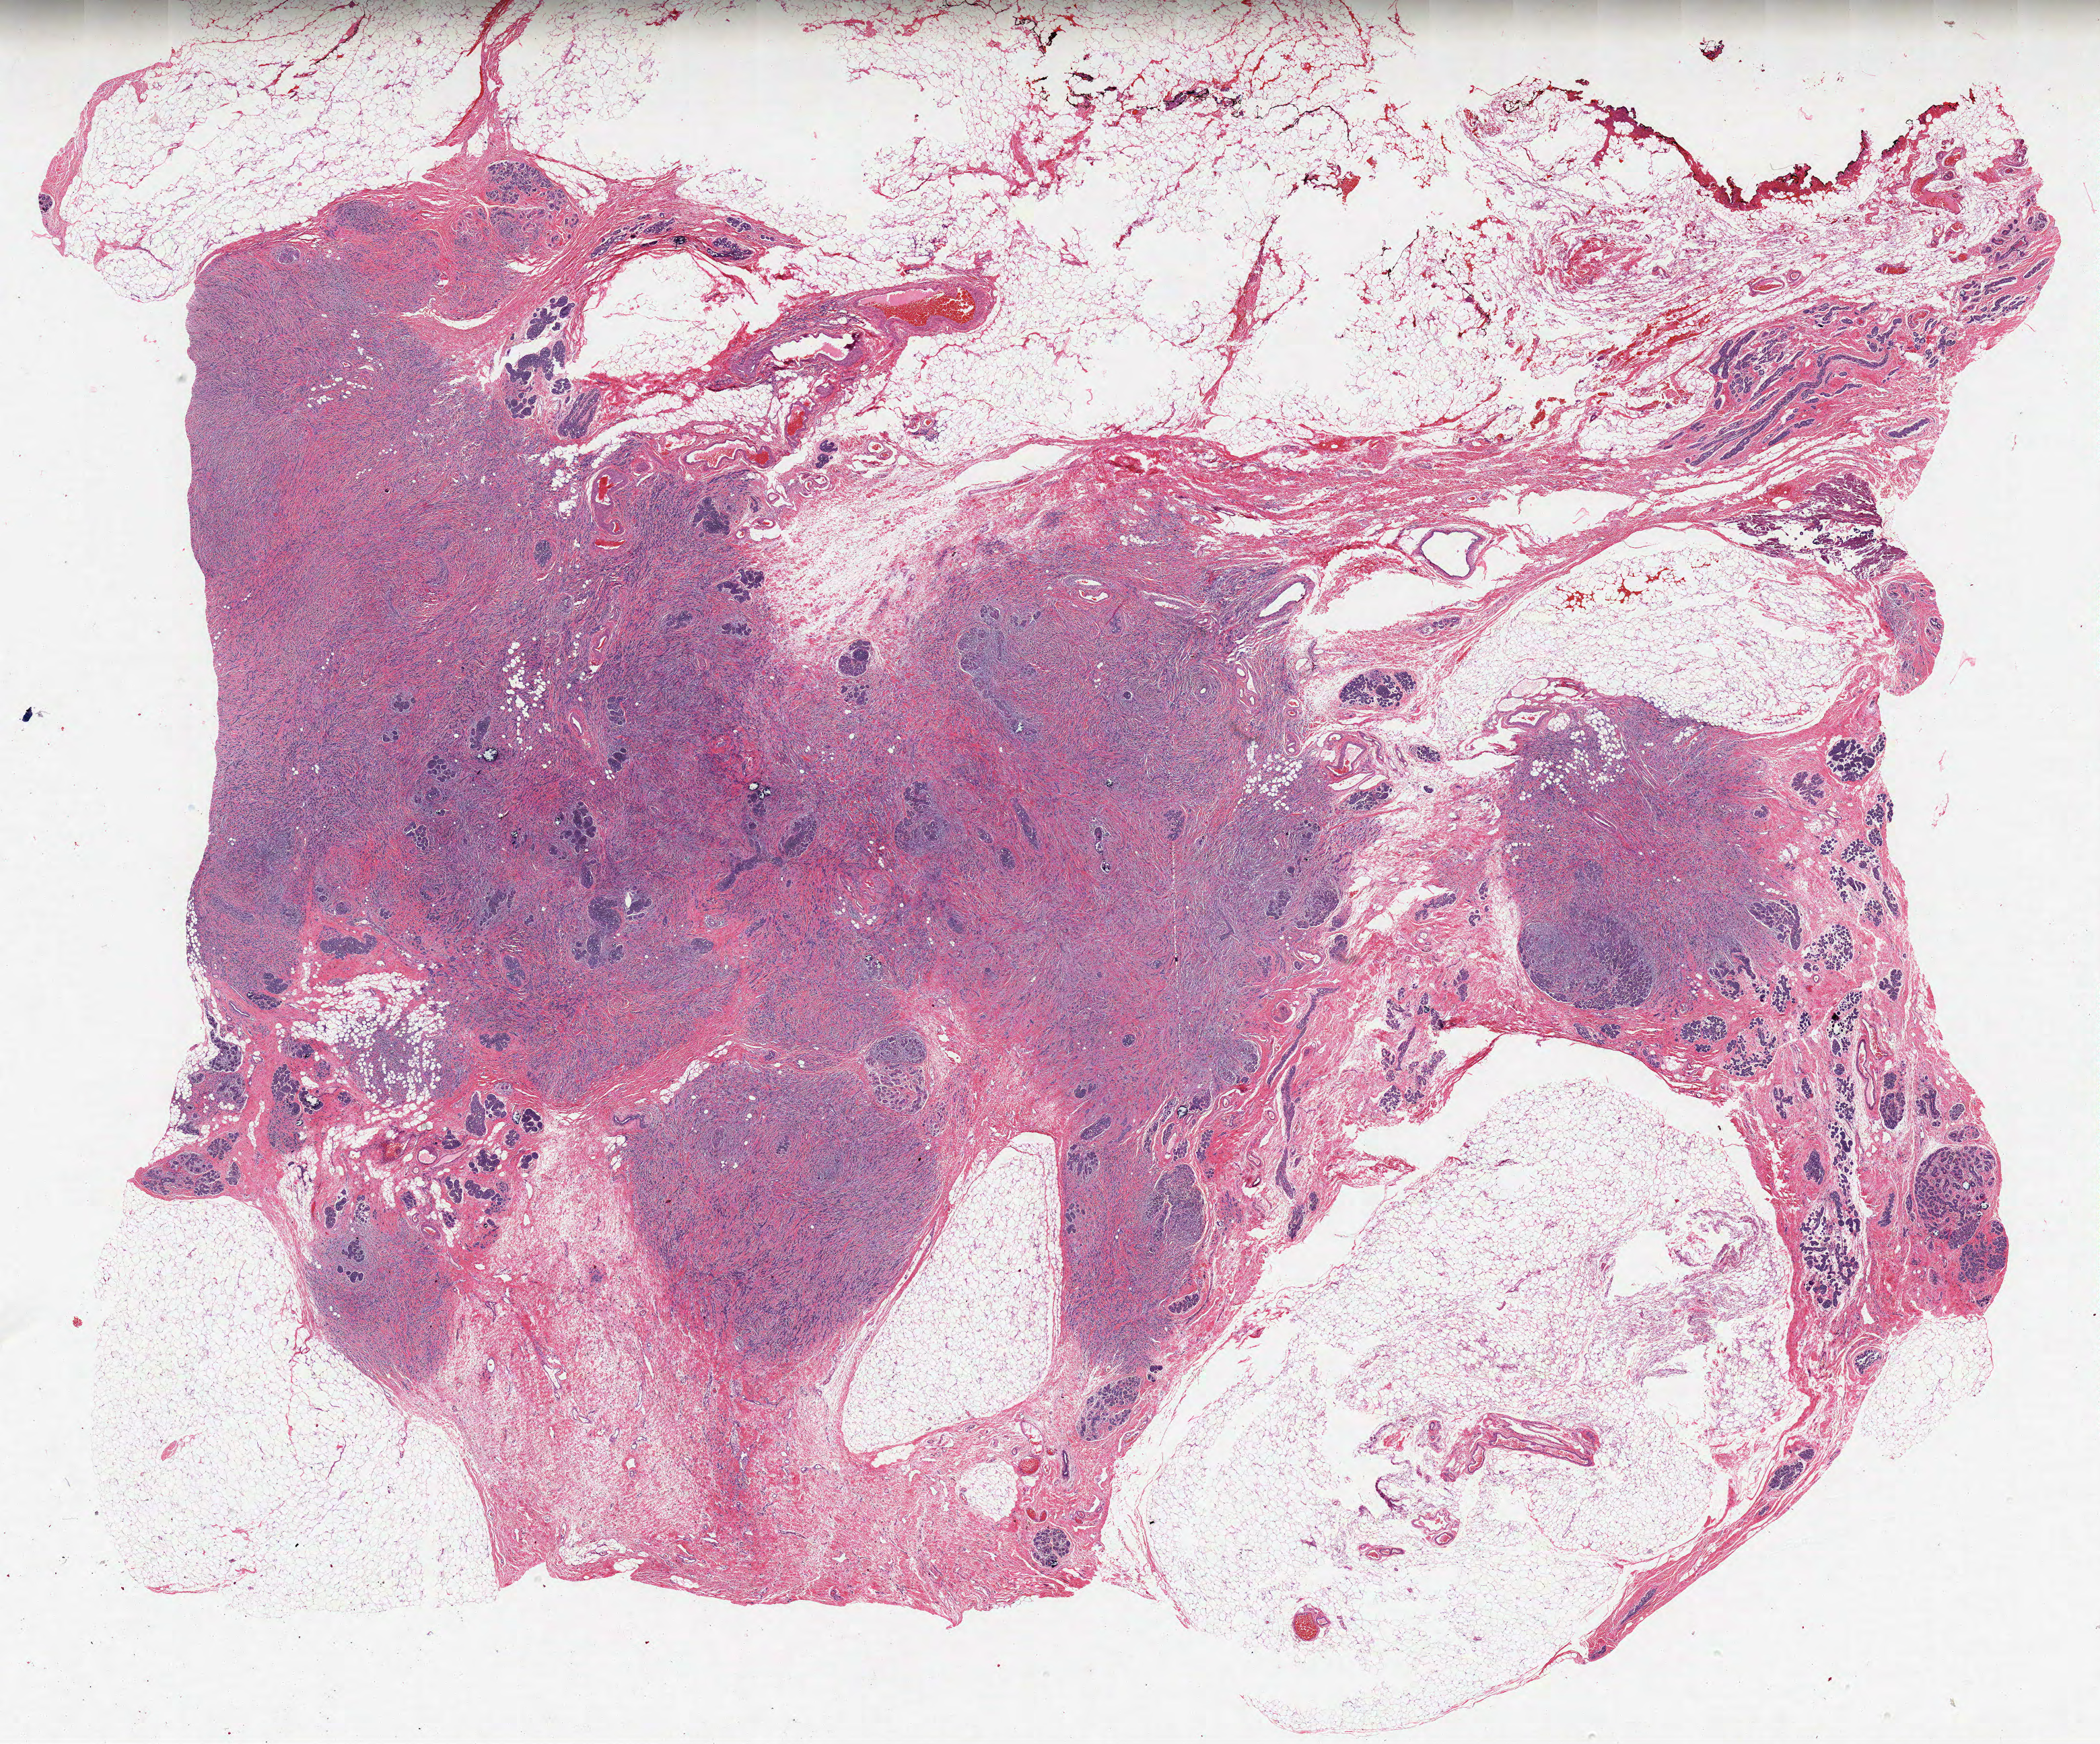
H&E whole-slide image, shown as a low-resolution overview of the whole scanned area (about 24.9 x 20.6 mm, acquisition: 20x scan); FFPE section; sample: primary tumour, breast. Female patient; age at initial diagnosis 46 years.
- TNM: T3 N0 (i+) M0
- lymph nodes positive (case pathology): 0 of 19 examined
- AJCC pathologic stage: IIB
- laterality: left
- diagnosis: Lobular carcinoma, NOS